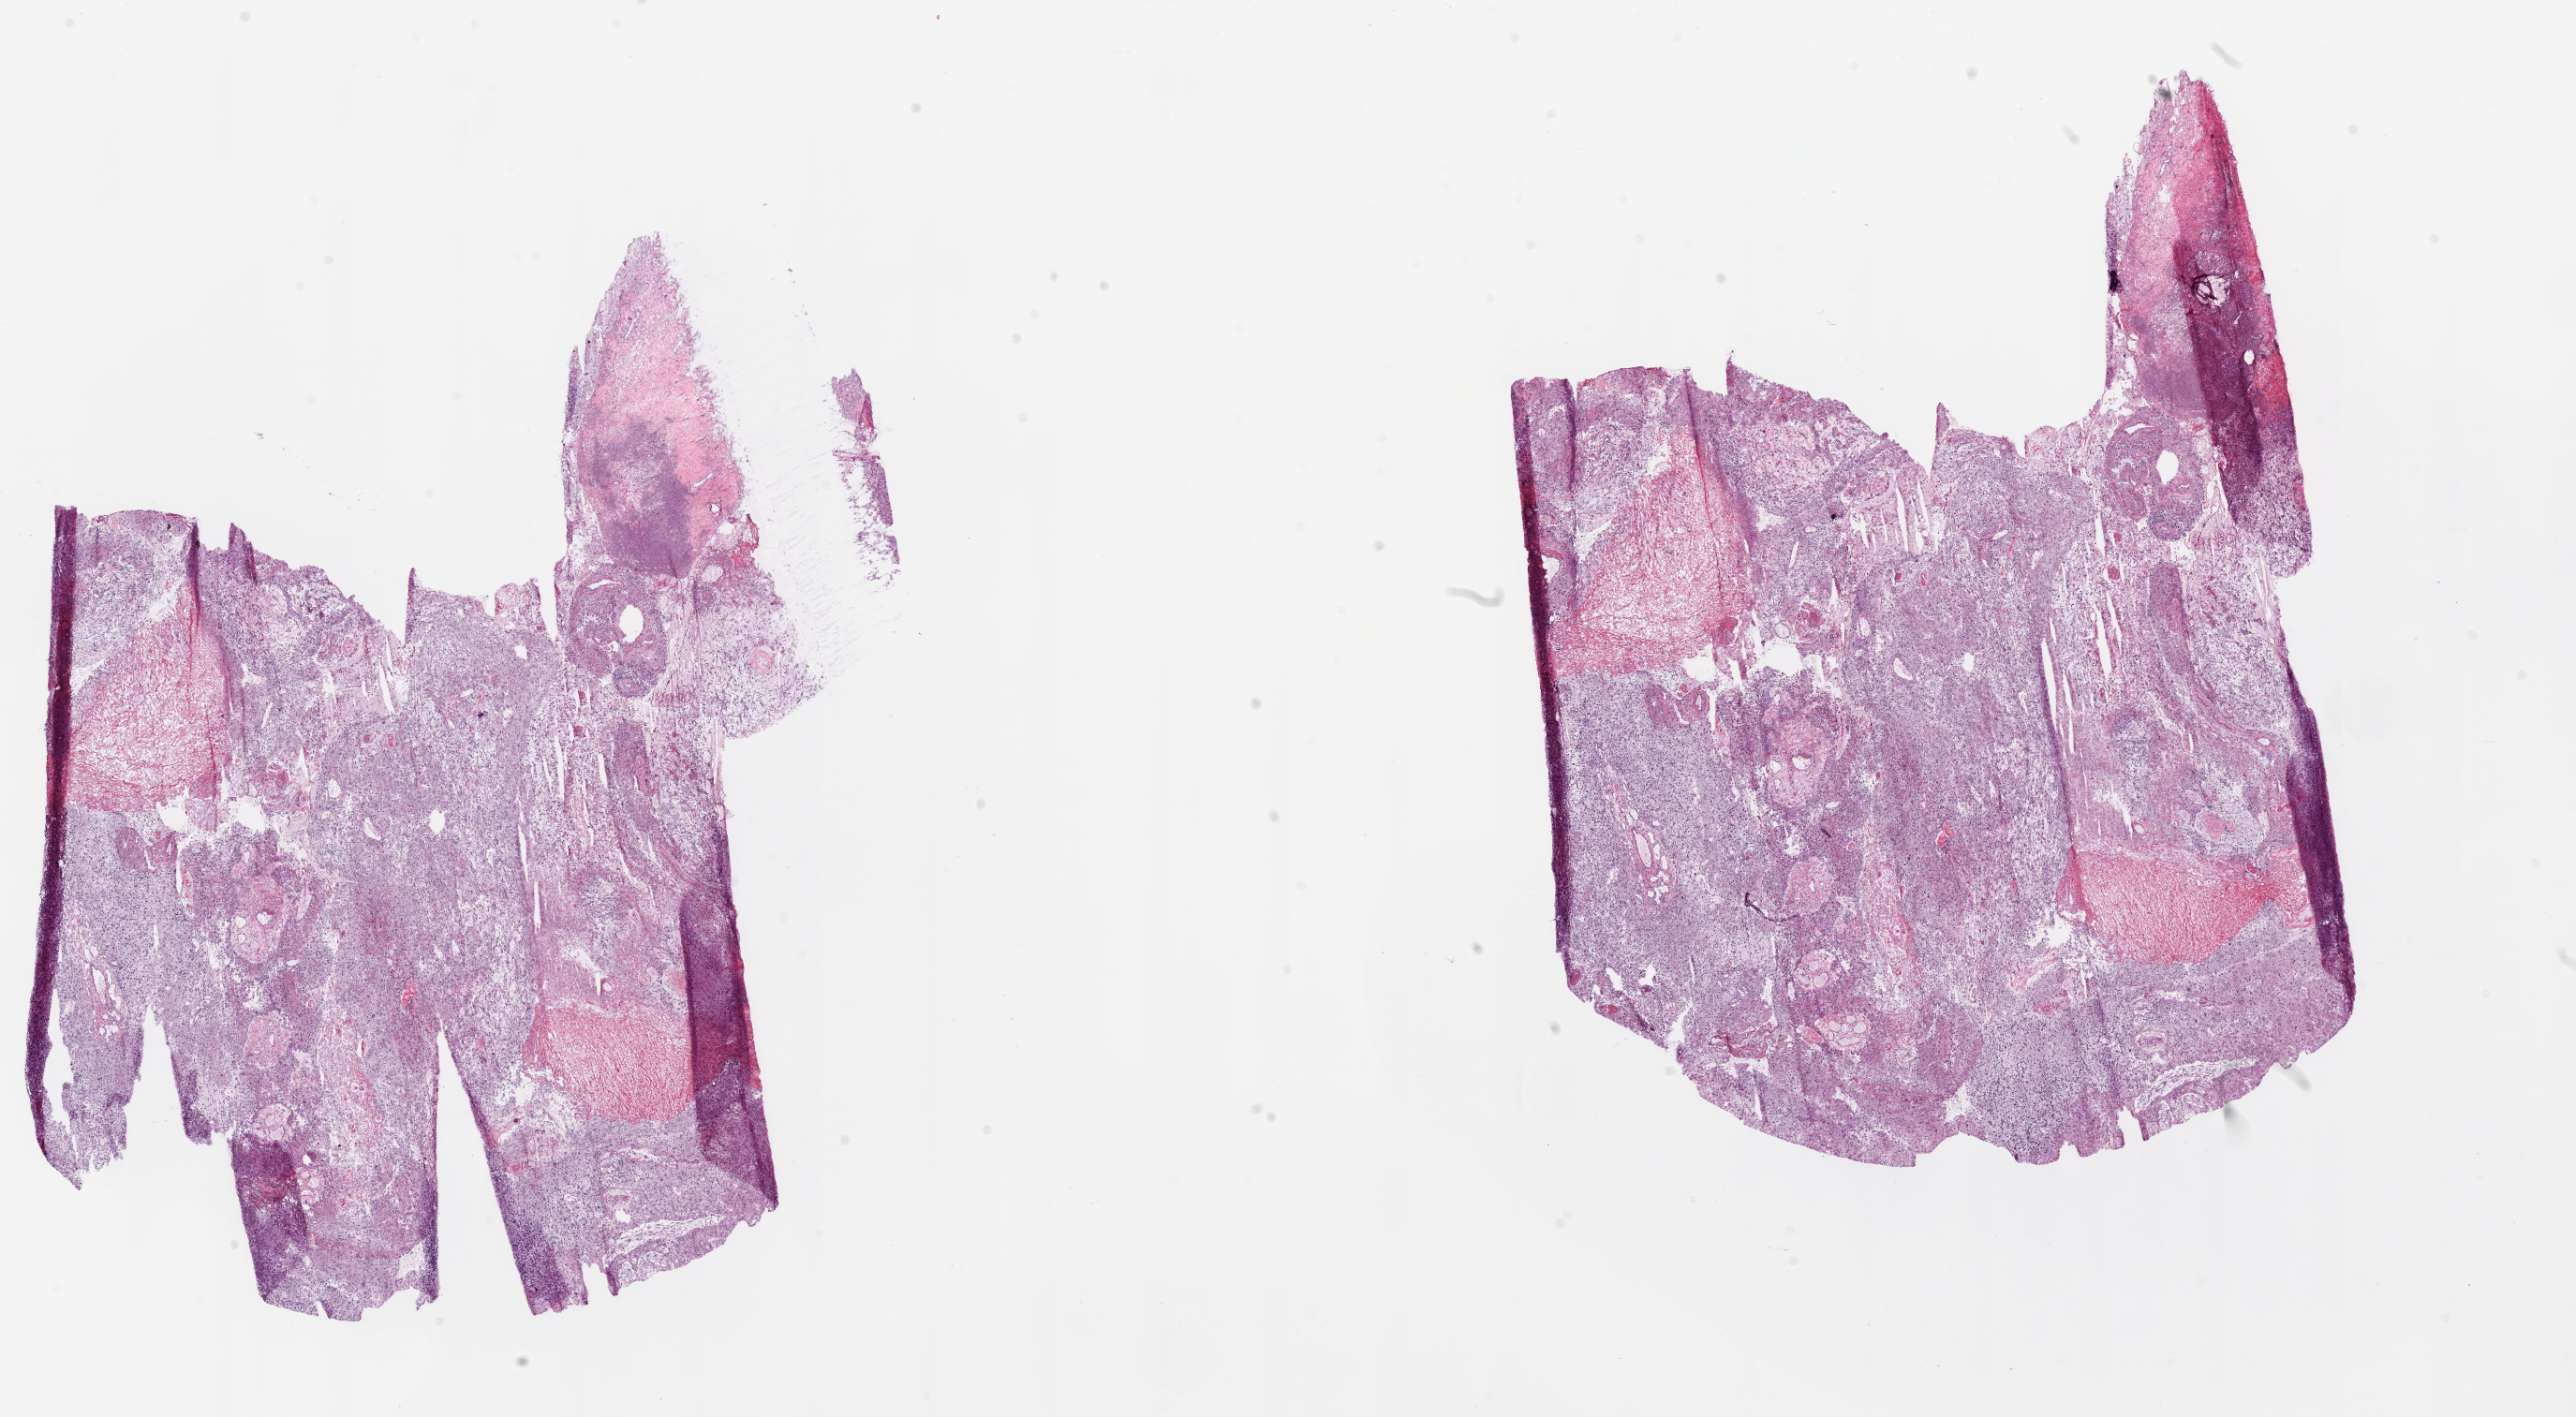
Digitized H&E-stained tissue section (whole slide), low-resolution overview of the scanned area, about 22.1 x 12.1 mm; frozen section; primary tumour sample from the brain. Male patient; age at initial diagnosis 48 years. Composition of this section per pathologist review: tumour cells 82%, tumour nuclei 80%, normal cells 0%, stromal cells 0%, necrosis 18%.
Histologic diagnosis: Glioblastoma.